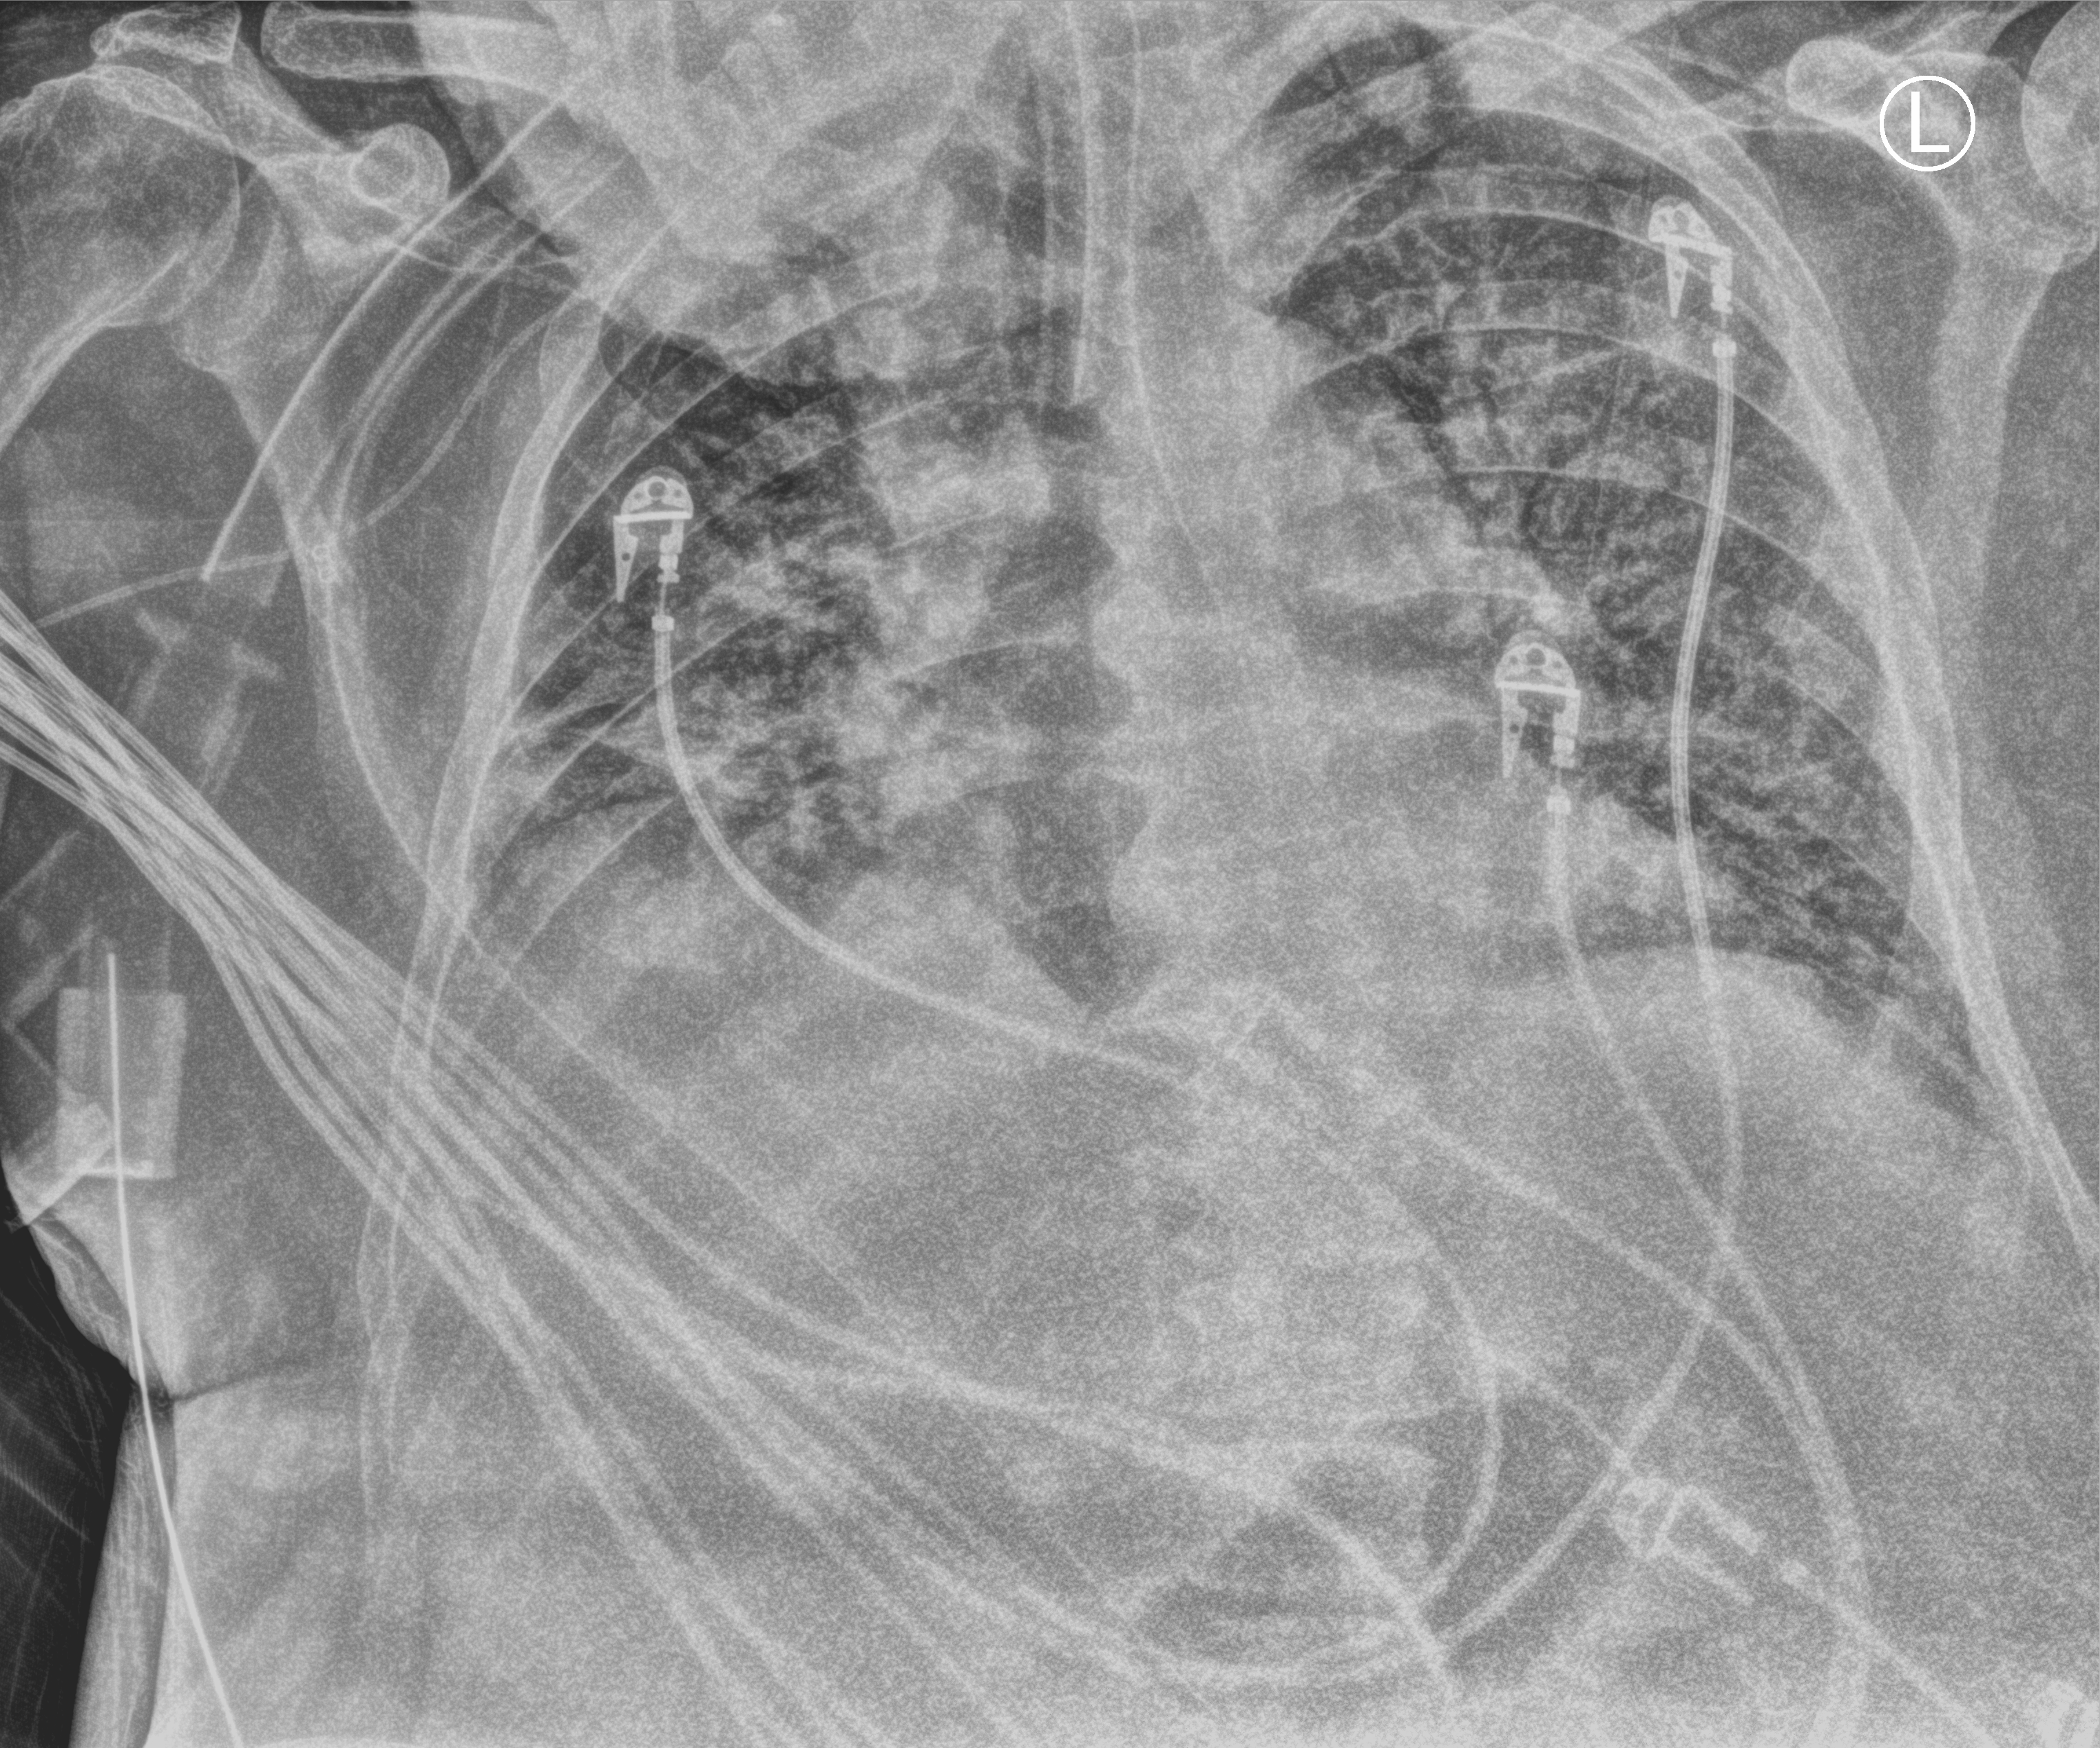
Chest X-ray (portable); anteroposterior (AP) projection. Patient hospitalised with COVID-19; male, aged 60–74 years.
Hospital-stay facts (about this admission, not read from this image; timing relative to this image not recorded): mechanically ventilated during this hospital stay: yes; admitted to intensive care during this hospital stay: yes.